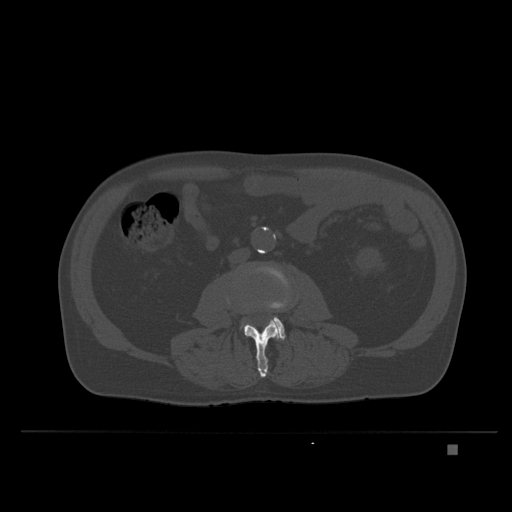
CT including the spine, one axial slice; slice 89 of 435 in the series (ordered by position); bone window (W 1800 / L 400 HU); 1.5 mm slice thickness; 512 × 512 image matrix. Patient: male, 73 years. From the clinical record (not read from this slice): primary cancer: skin.
Outlined on this slice (semi-automatically segmented with operator editing):
- L3 vertebra: bounding box (x1, y1, x2, y2) in pixels: (244, 320, 281, 378)
- L4 vertebra: (244, 269, 292, 340)